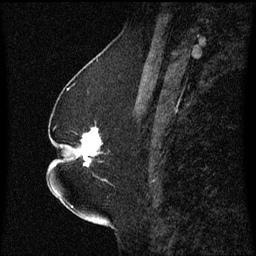
Breast MRI (dynamic contrast-enhanced), one sagittal slice. Dynamic contrast-enhanced series, image 2 of 3 at this slice position (ordered by acquisition). 1.5 T. TE 4.2 ms, TR 8.4 ms. 2.3 mm slice thickness. 256 × 256 image matrix, field of view 200 × 200 mm. Patient: female, 52 years. From the clinical record (not read from this slice): setting: breast cancer imaged before/during neoadjuvant chemotherapy; receptor status: HR-positive, HER2-negative.
Annotated regions visible in this slice (semi-automatically segmented with operator editing):
- analysis volume of interest (the breast-tissue region the enhancement analysis was run in; not a lesion): bounding box (x1, y1, x2, y2) in pixels: (65, 128, 109, 183)
- tumour enhancement mask (voxels above the 70 % enhancement threshold inside the analysis volume of interest): (77, 128, 102, 167)